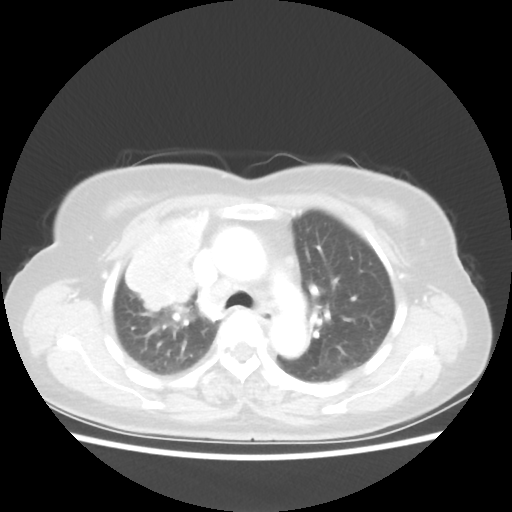
Chest CT, one axial slice; slice 37 of 55 in the series (ordered by position); reconstruction kernel STANDARD; 80 kVp; lung window (W 1500 / L -600 HU); 5 mm slice thickness; 512 × 512 image matrix, field of view 337 × 337 mm. Female patient, age 62 years. Case-level facts recorded for this patient, not image findings: clinical TNM (as recorded): T4 N3 M0.
Annotated regions visible in this slice (bounding box drawn by a radiologist):
- lung tumour (recorded histology: squamous cell carcinoma): box from (x=117, y=205) to (x=214, y=319) px